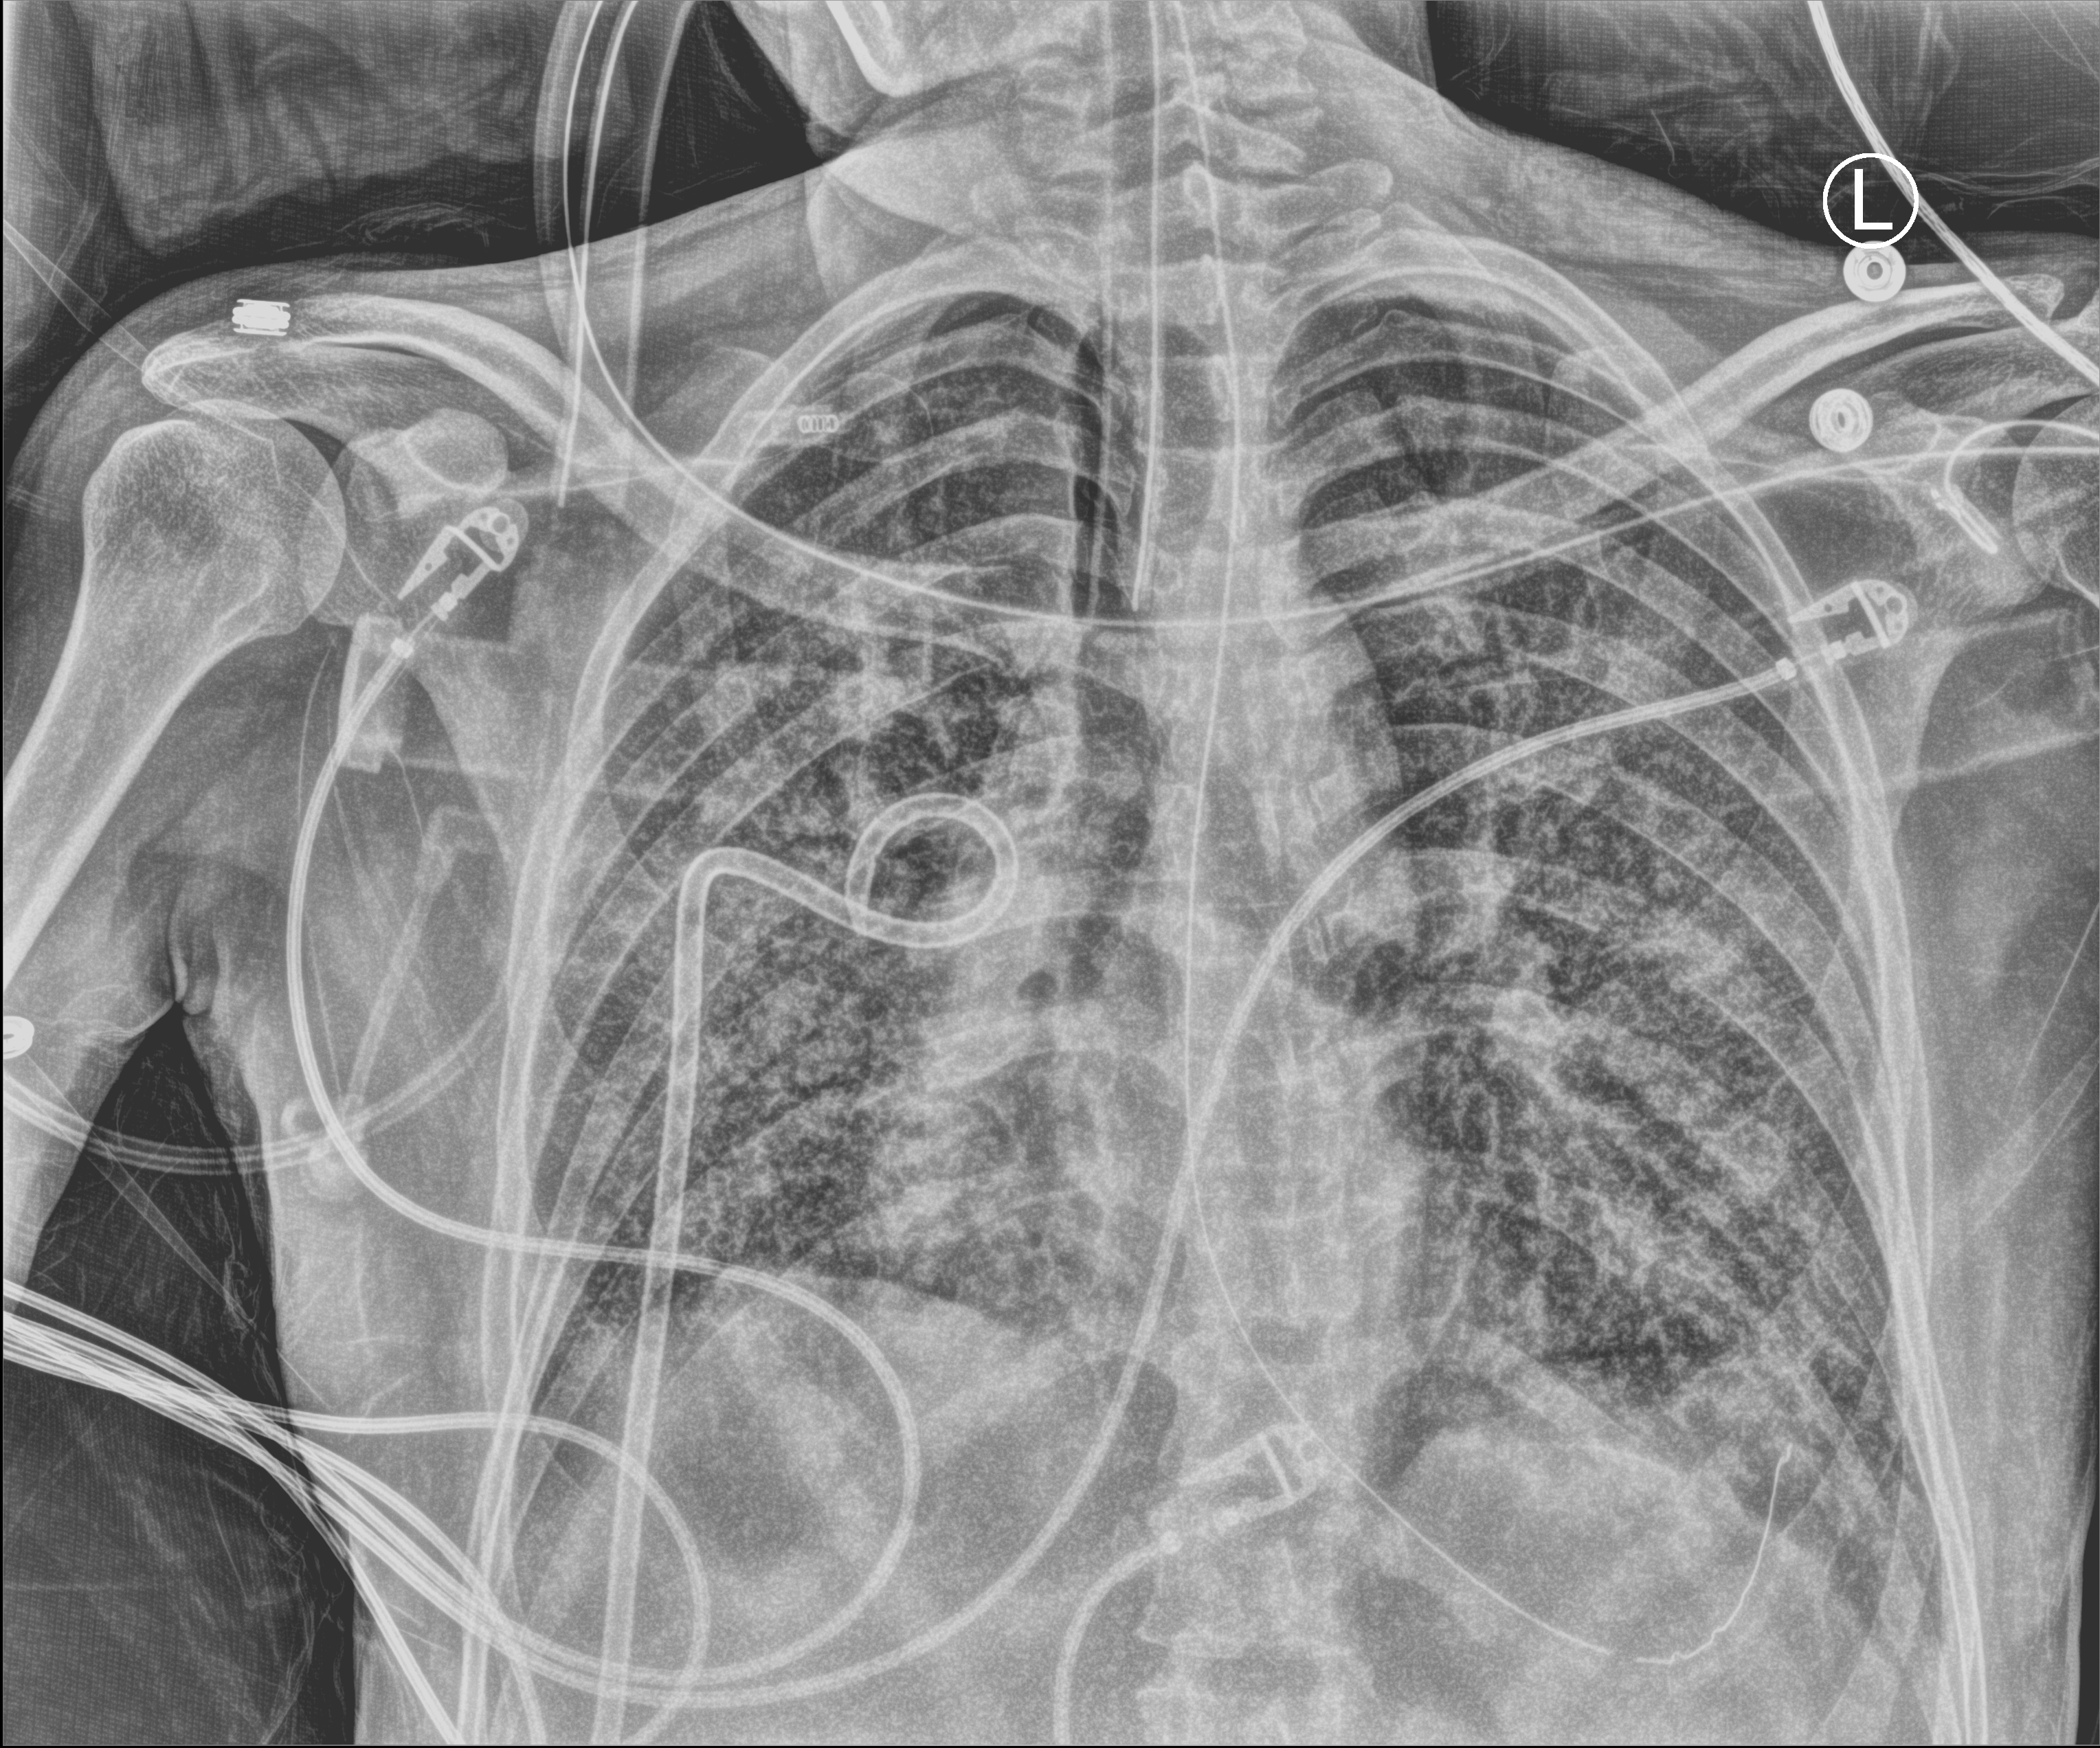
Portable chest radiograph; anteroposterior (AP) projection. Adult patient hospitalised with COVID-19, age 18–59 years.
From the hospital-stay record, not from the radiograph (when in the stay this image was taken is not recorded): mechanically ventilated during this hospital stay: yes; admitted to intensive care during this hospital stay: yes.